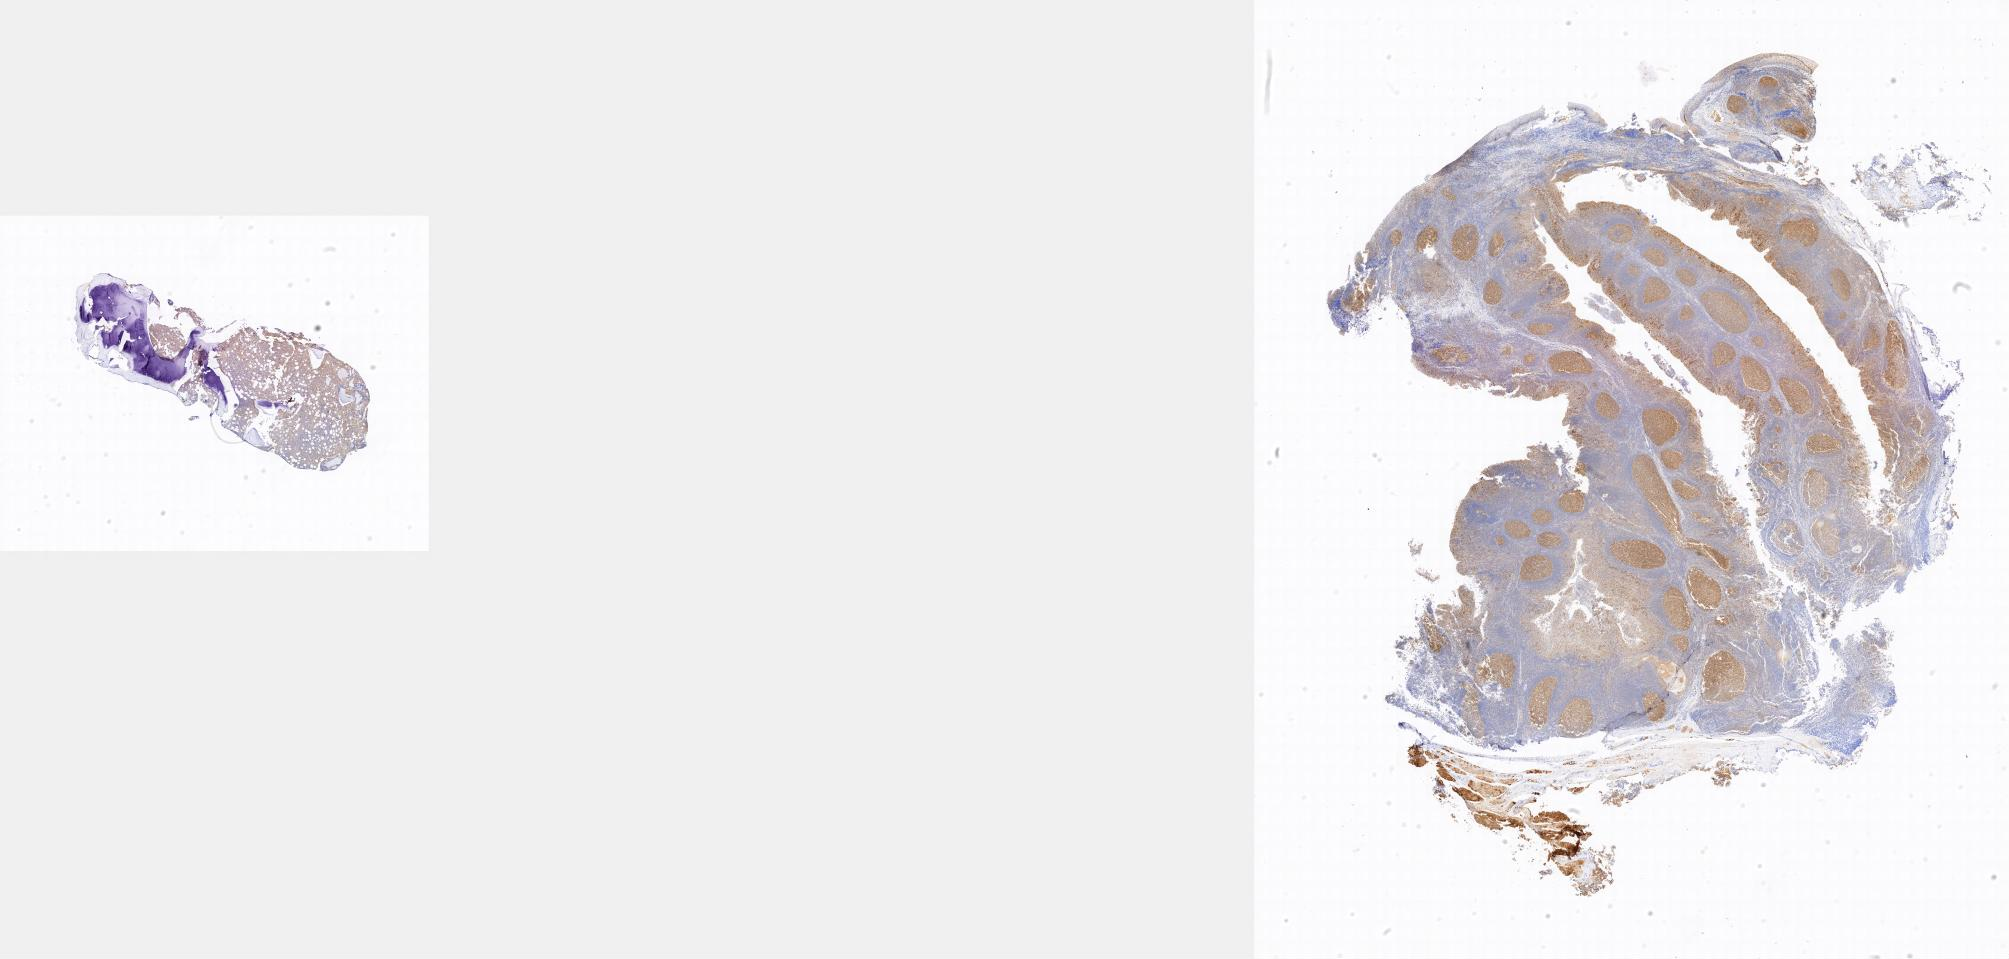
Whole-slide image, immunohistochemical stain for BCL6 — low-resolution overview of the scanned area; specimen: tumor tissue; anatomic site: bone marrow. Patient male; aged 15.
Diagnosis: Burkitt lymphoma, NOS.